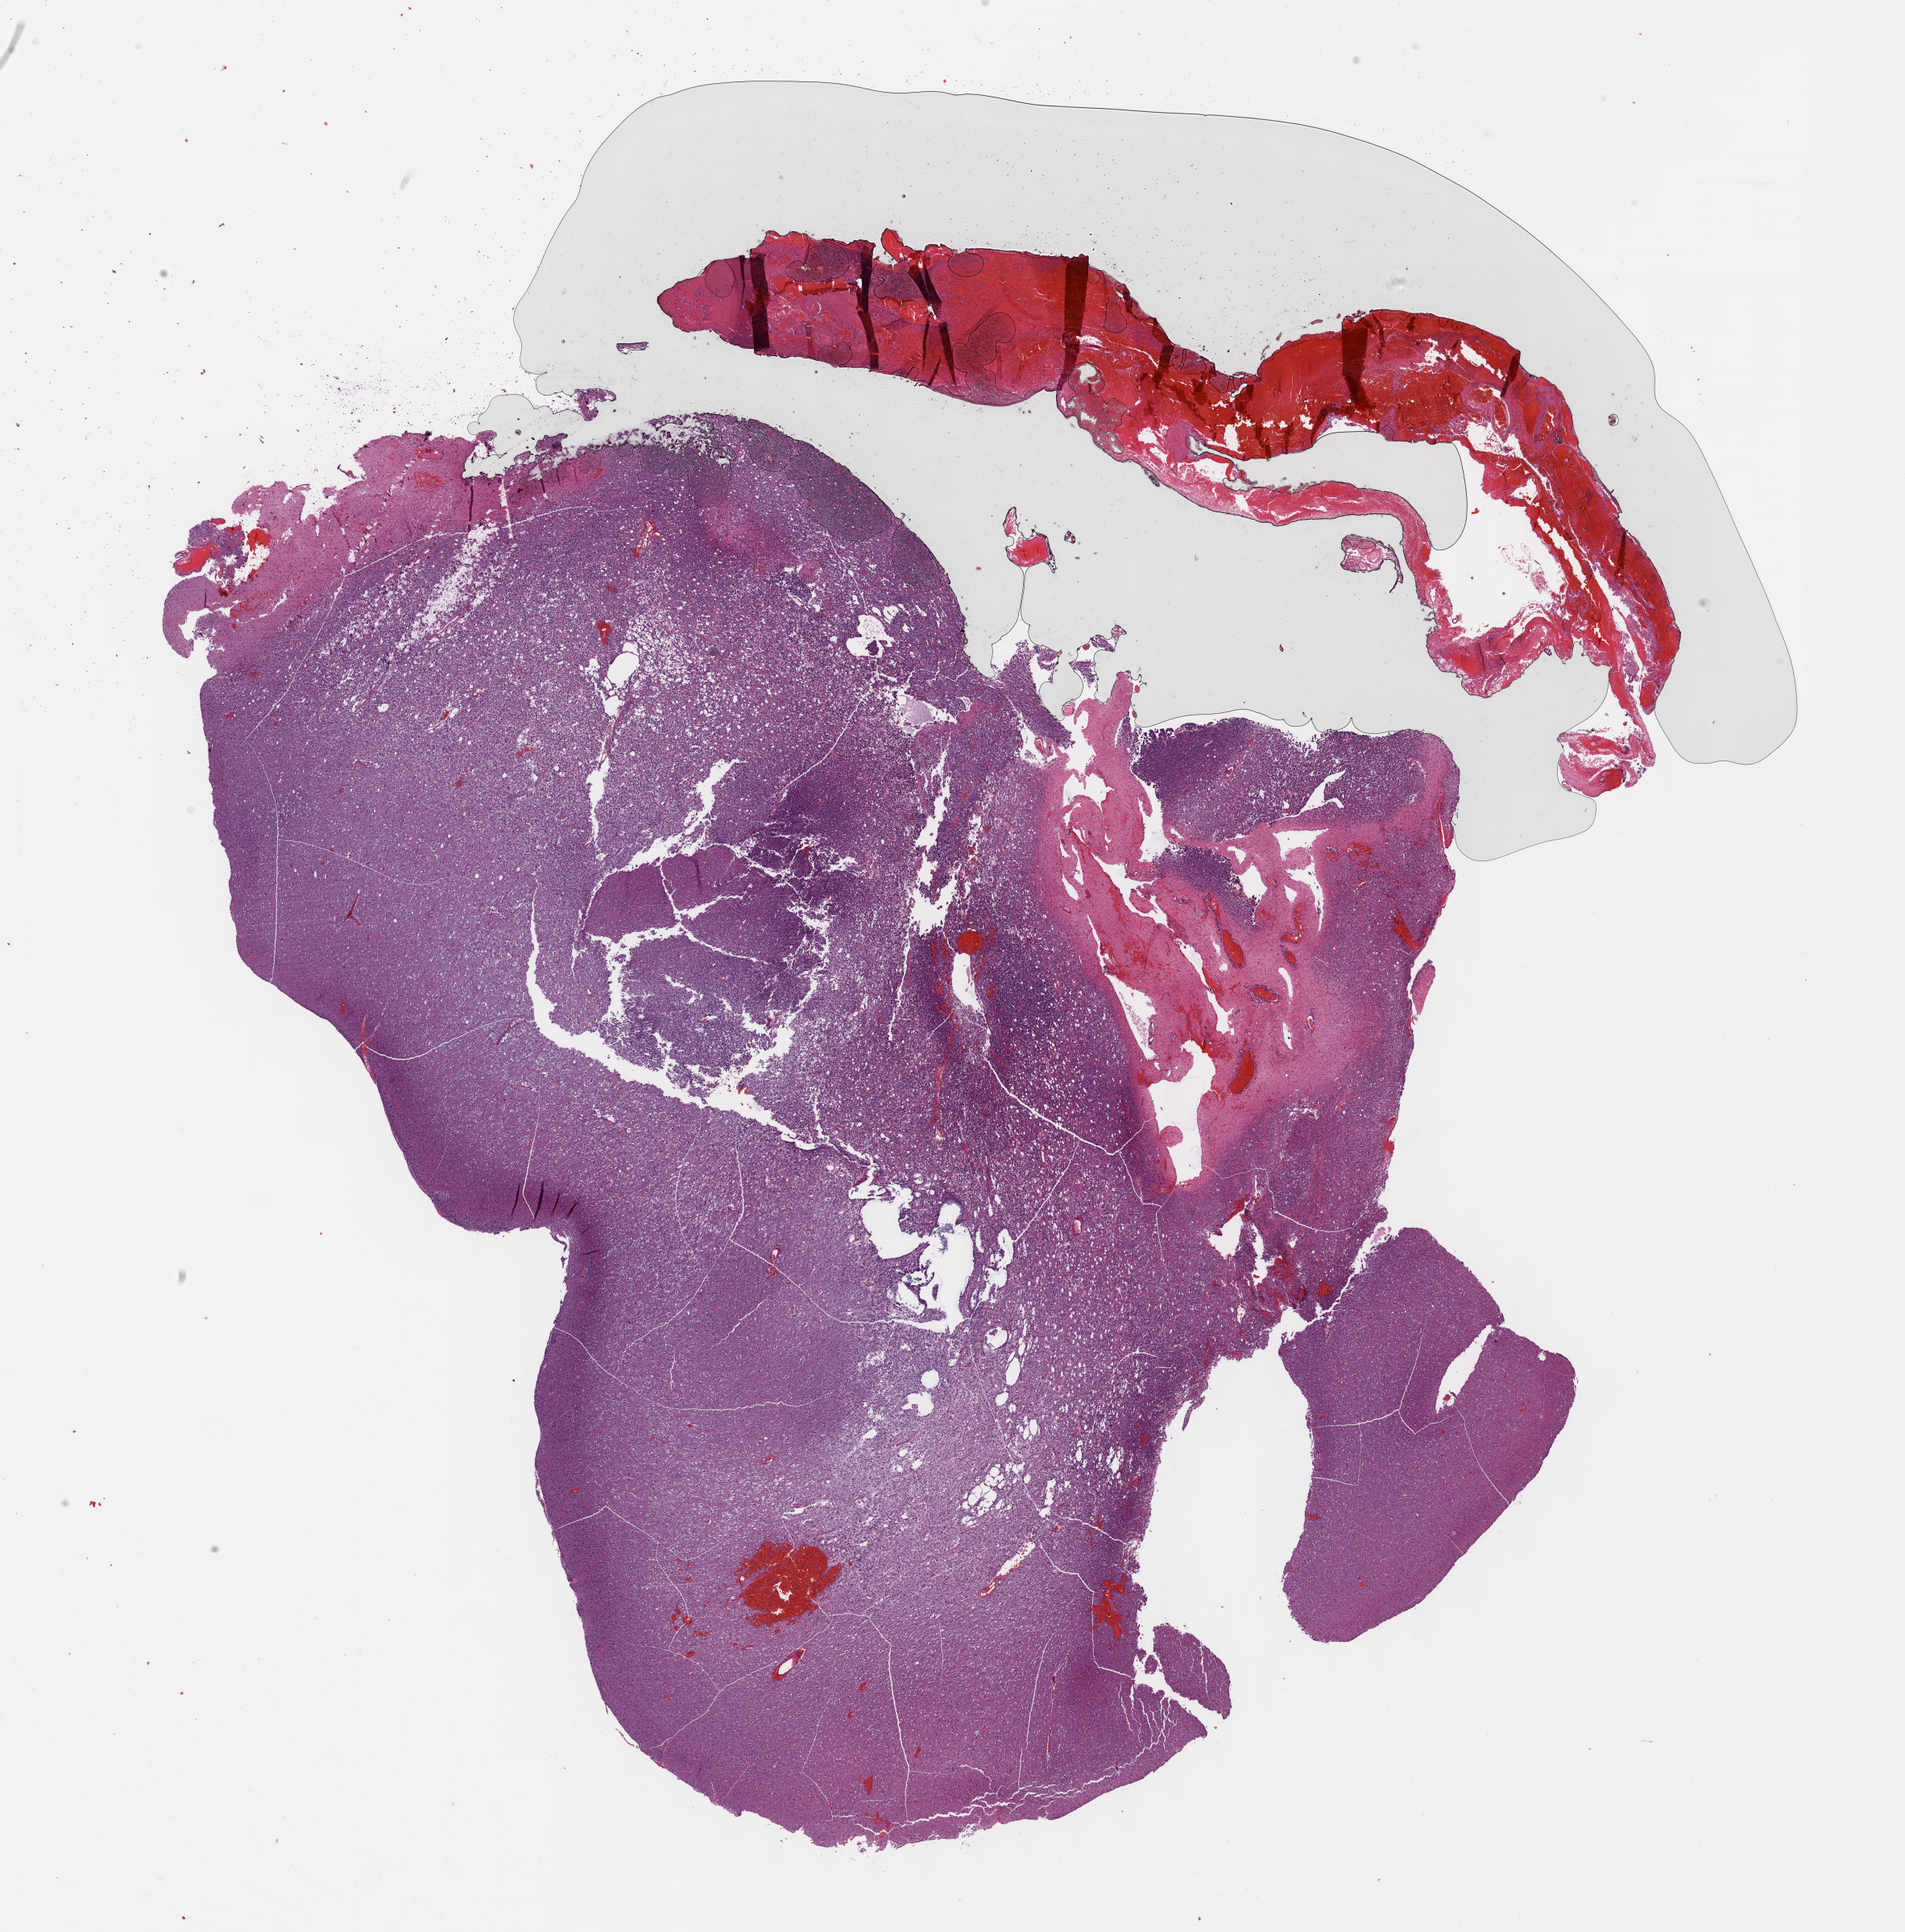
Whole-slide histology image, H&E-stained — low-resolution overview of the scanned area, about 19.1 x 19.4 mm (acquisition: 40x scan), FFPE section, brain, primary tumour sample. Male, age 35 years at initial diagnosis.
Pathologic diagnosis: Oligodendroglioma, anaplastic.